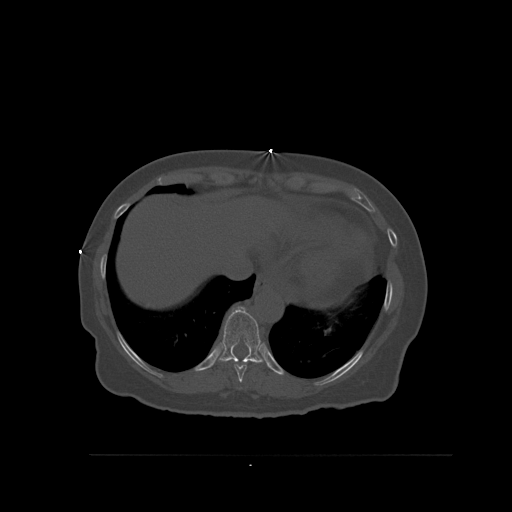
CT including the spine, one axial slice. Slice 324 of 527 in the series (ordered by position). Bone window (W 1800 / L 400 HU). 1.5 mm slice thickness. 512 × 512 image matrix, field of view 470 × 470 mm. Female patient, age 73 years. From the clinical record (not read from this slice): primary cancer: breast; vertebrae with lytic lesions (as recorded): L2.
Annotated regions visible in this slice (semi-automatic segmentation, software-assisted and operator-edited):
- T10 vertebra: bounding box (x1, y1, x2, y2) in pixels: (213, 306, 264, 365)
- T9 vertebra: (234, 362, 247, 383)